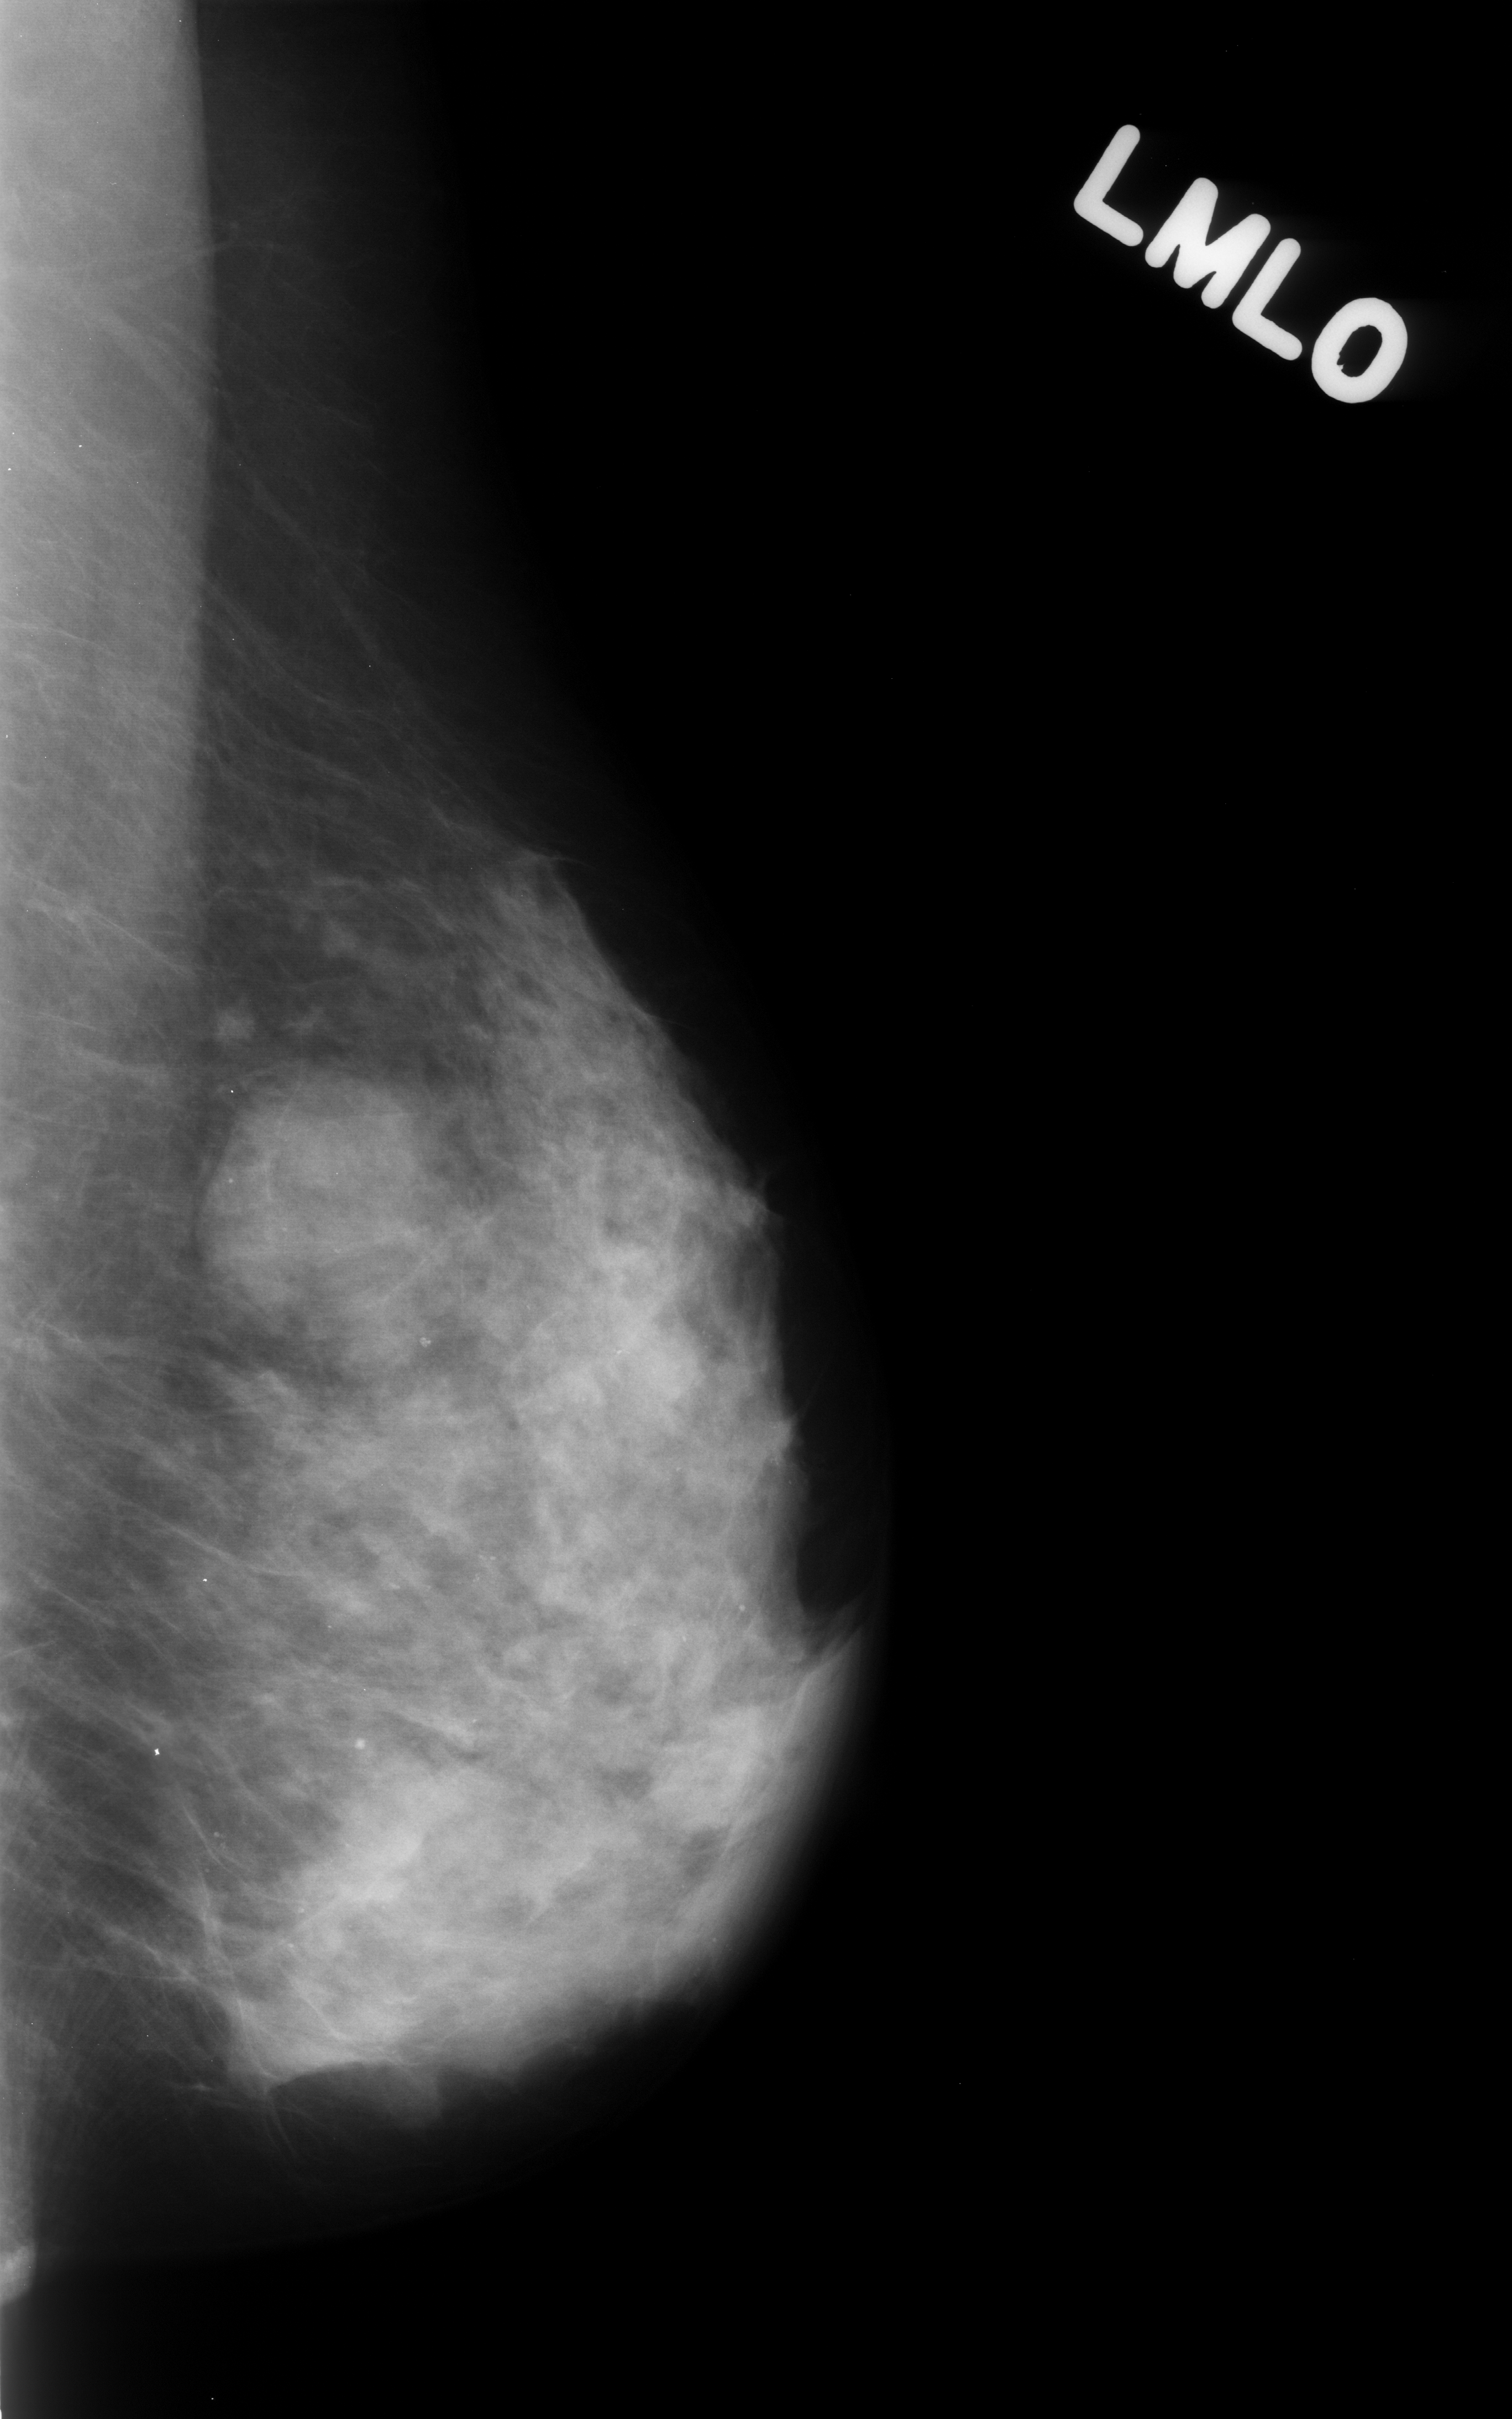
Digitized screen-film mammogram; left breast; MLO view; breast composition: heterogeneously dense (BI-RADS density category 3 of 4); 1512 × 2419 image matrix.
Expert-marked regions of interest on this image (one box per marked abnormality):
- mass, shape lobulated, margins obscured; BI-RADS assessment category 4; pathology result (as recorded, not read from the image): benign: bounding box (x1, y1, x2, y2) in pixels: (206, 1093, 433, 1317)